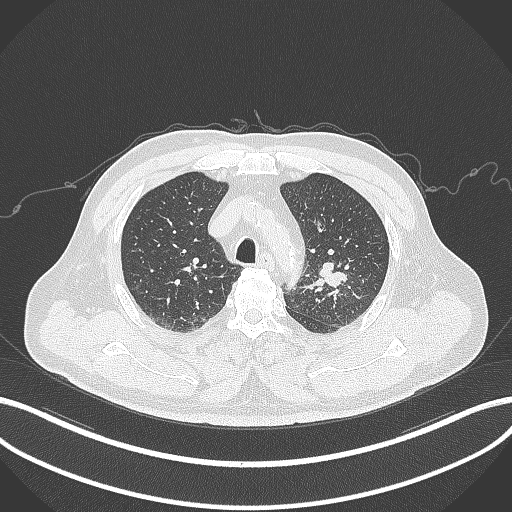
Chest CT, one axial slice; position 235 of 286 along the scan axis; reconstruction kernel B70f; 120 kVp; lung window (W 1500 / L -600 HU); 512 × 512 image matrix, field of view 400 × 400 mm. Male patient, age 67 years. From the clinical record (not read from this slice): clinical TNM (as recorded): T2a N1 M0; histopathological grade: G3.
Annotated regions visible in this slice (bounding box drawn by a radiologist):
- lung tumour (recorded histology: adenocarcinoma): box from (x=315, y=257) to (x=350, y=291) px